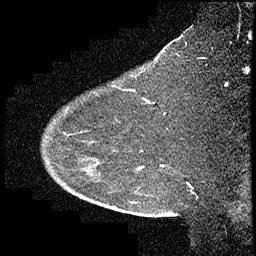
Breast MRI (dynamic contrast-enhanced), one sagittal slice. Slice 203 of 232 in the series (ordered by position). Dynamic contrast-enhanced study with each time point stored as its own series, time point 2 of 4 at this slice position (early post-contrast, ordered by acquisition time). 1.5 T. TE 4.2 ms, TR 6.7 ms. 3 mm slice thickness. 256 × 256 image matrix, field of view 200 × 200 mm. Patient: female, 63 years. Case-level facts recorded for this patient, not image findings: setting: breast cancer imaged before/during neoadjuvant chemotherapy; receptor status: triple-negative.
Outlined on this slice (semi-automatic segmentation, software-assisted and operator-edited):
- analysis volume of interest (the breast-tissue region the enhancement analysis was run in; not a lesion): box from (x=42, y=90) to (x=140, y=211) px
- tumour enhancement mask (voxels above the 70 % enhancement threshold inside the analysis volume of interest): (x=138, y=168)–(x=140, y=170)